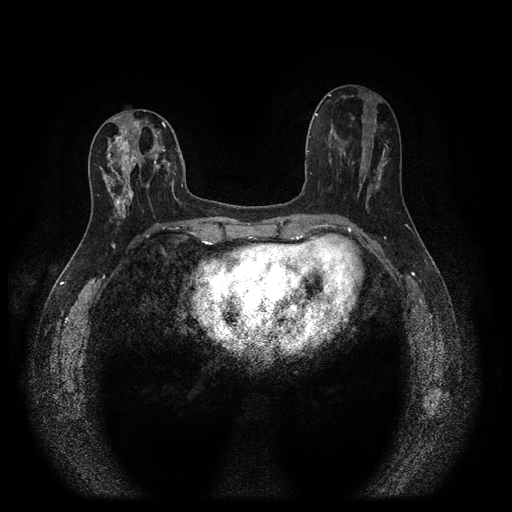
Breast MRI (dynamic contrast-enhanced, multi-phase), one axial slice. Slice 45 of 116 in the series (ordered by position). Dynamic contrast-enhanced series, time point 2 of 5 at this slice position (early post-contrast). 1.5 T. TE 2.7 ms, TR 5.4 ms. 512 × 512 image matrix. Patient: female, 47 years.
Annotated regions visible in this slice (semi-automatic segmentation, software-assisted and operator-edited):
- breast lesion (labelled 'tumour' in the annotation; benign lesions carry a separate 'benign' label): bounding box [x1, y1, x2, y2] px = [100, 122, 168, 219]